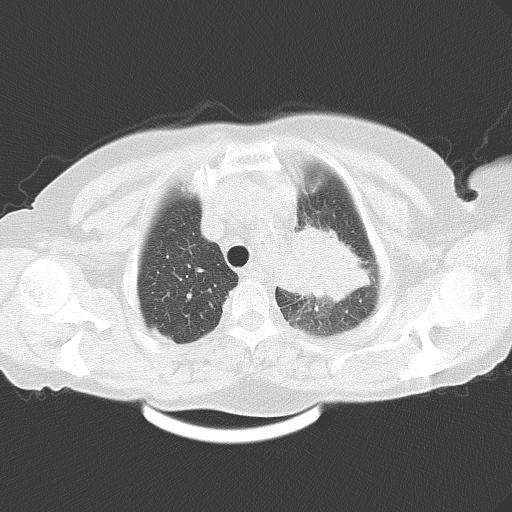
Chest CT, one axial slice; slice 44 of 54 in the series (ordered by position); lung window (W 1500 / L -600 HU); 5 mm slice thickness; 512 × 512 image matrix, field of view 353 × 353 mm. Female patient, age 71 years. Case-level facts recorded for this patient, not image findings: clinical TNM (as recorded): T3 N3 M0.
Outlined on this slice (bounding box drawn by a radiologist):
- lung tumour (recorded histology: adenocarcinoma): bounding box (x1, y1, x2, y2) in pixels: (287, 219, 381, 307)